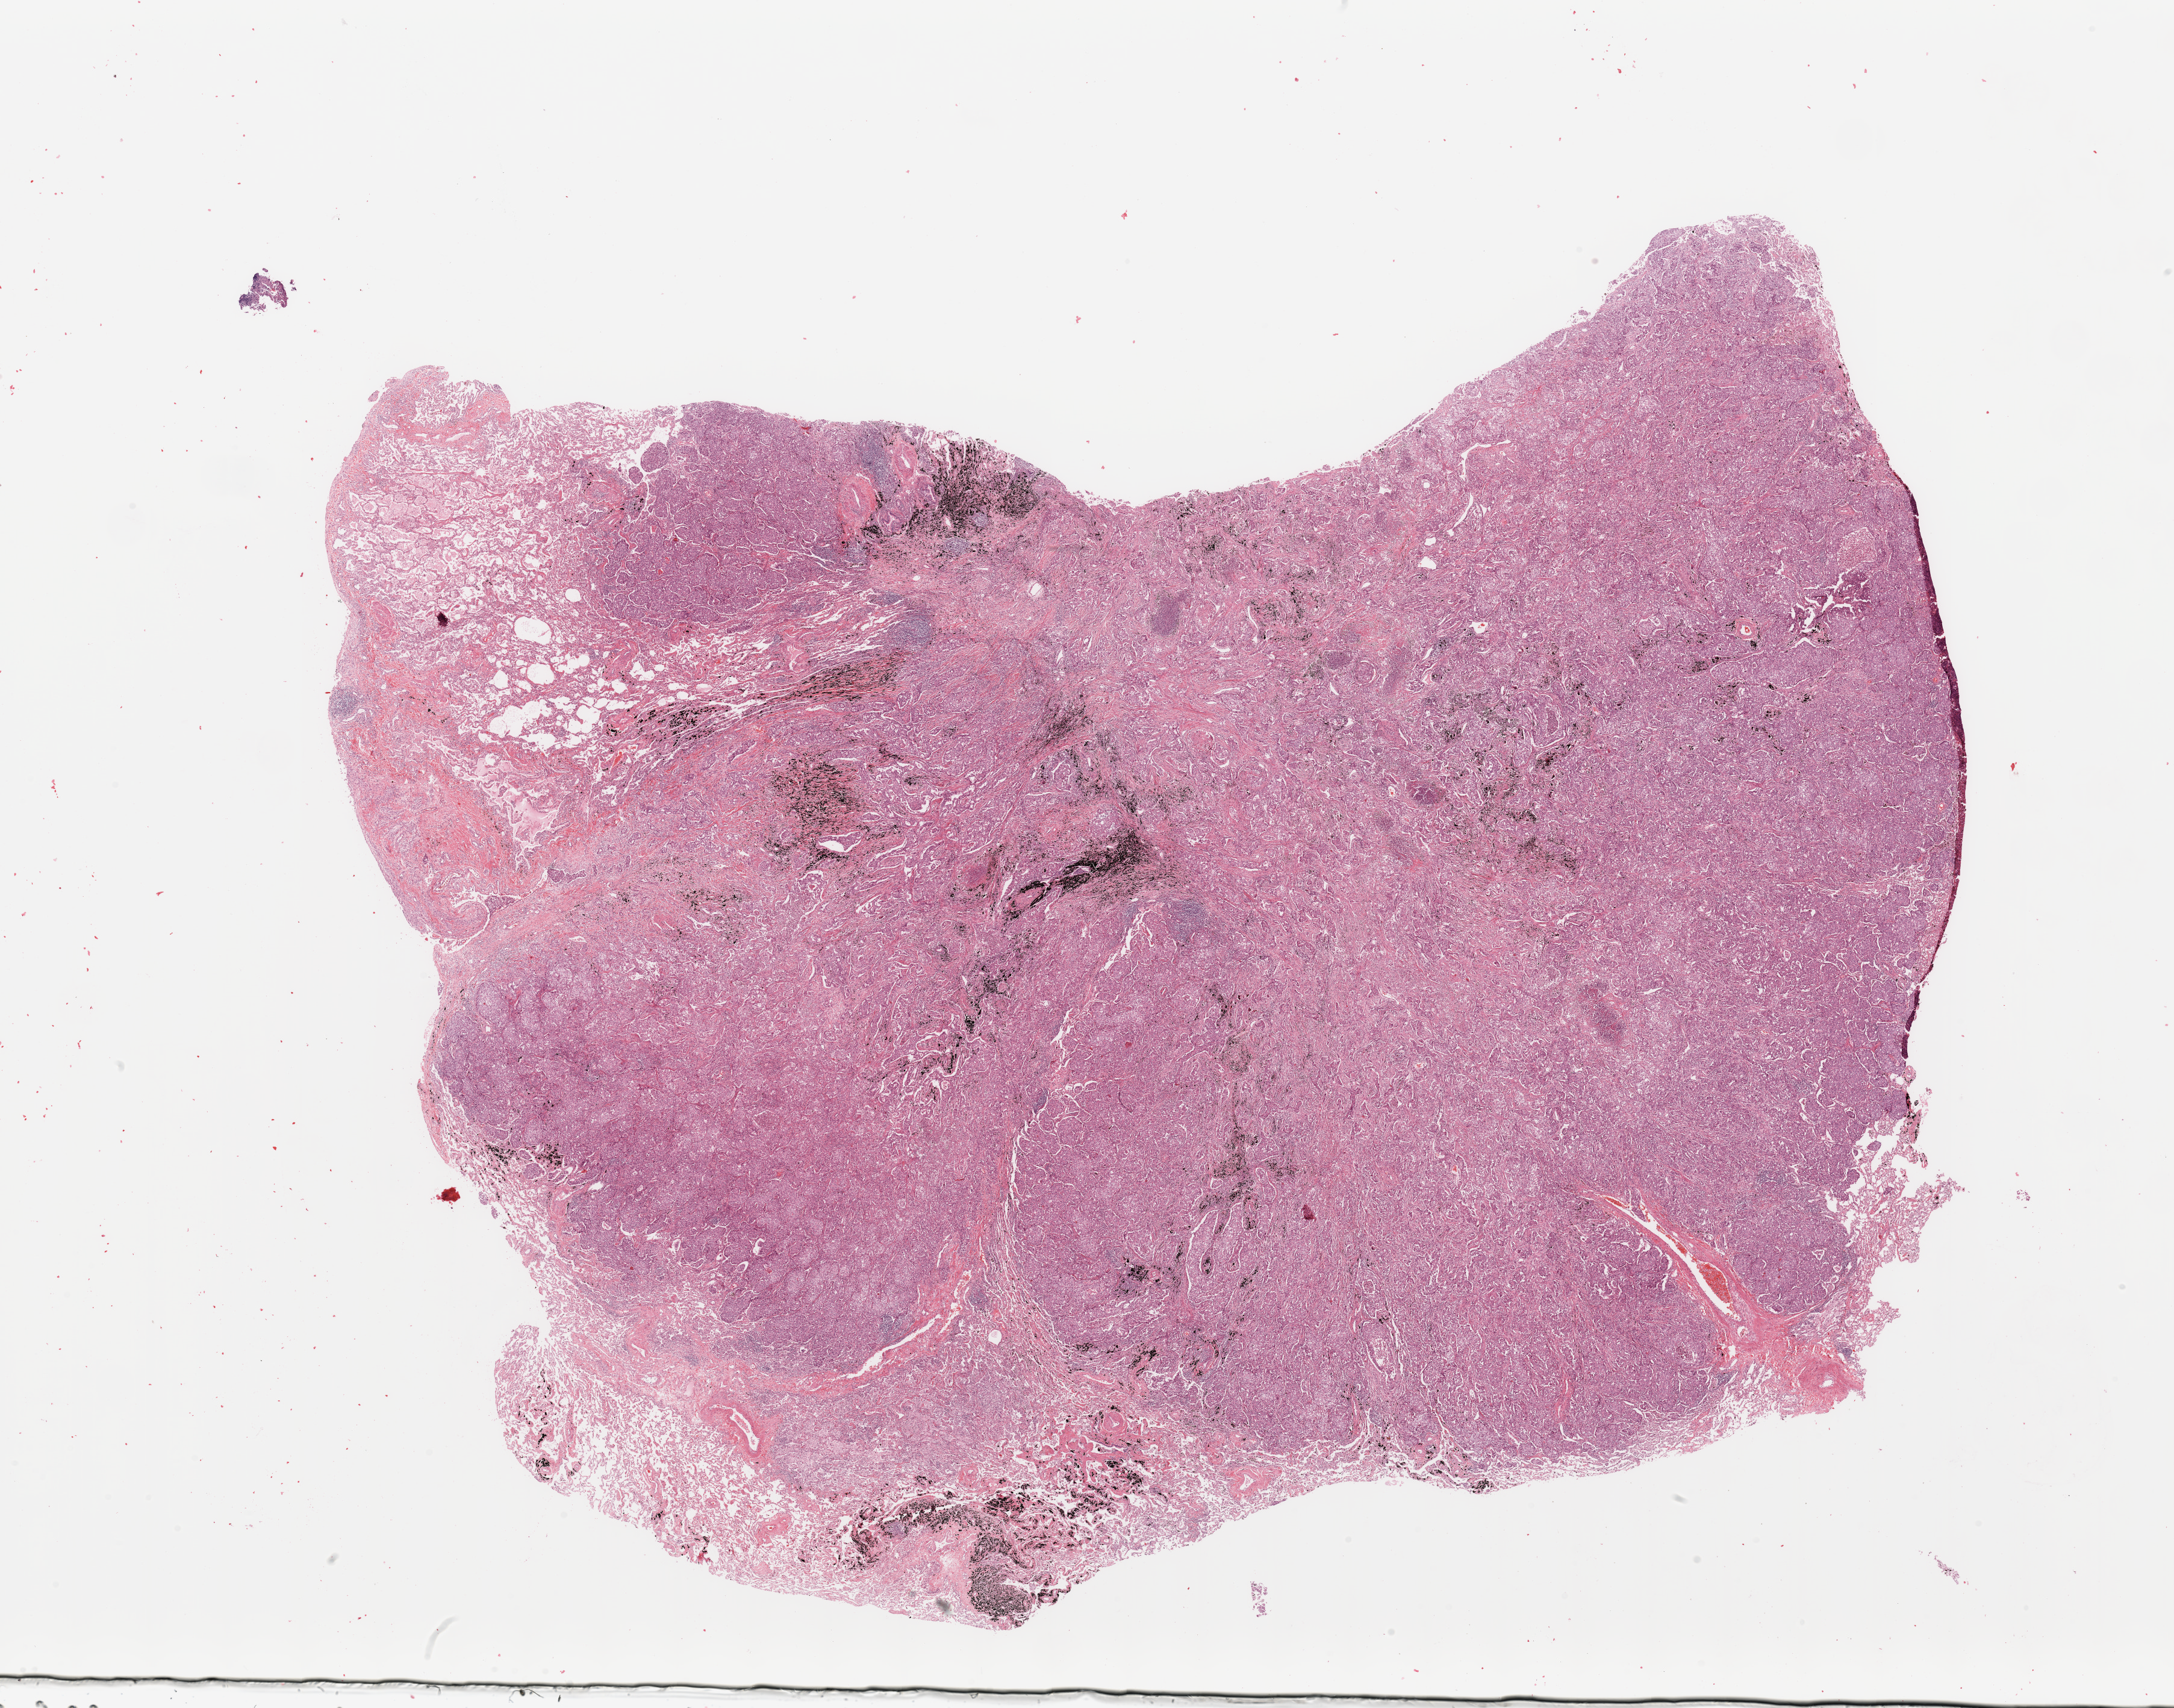
Whole-slide histology image, H&E — shown as a low-resolution overview of the whole scanned area (about 28.5 x 22.4 mm, from a 20x scan), lung, tumour tissue. Male, 54 y/o.
Diagnosis: Adenocarcinoma, NOS.